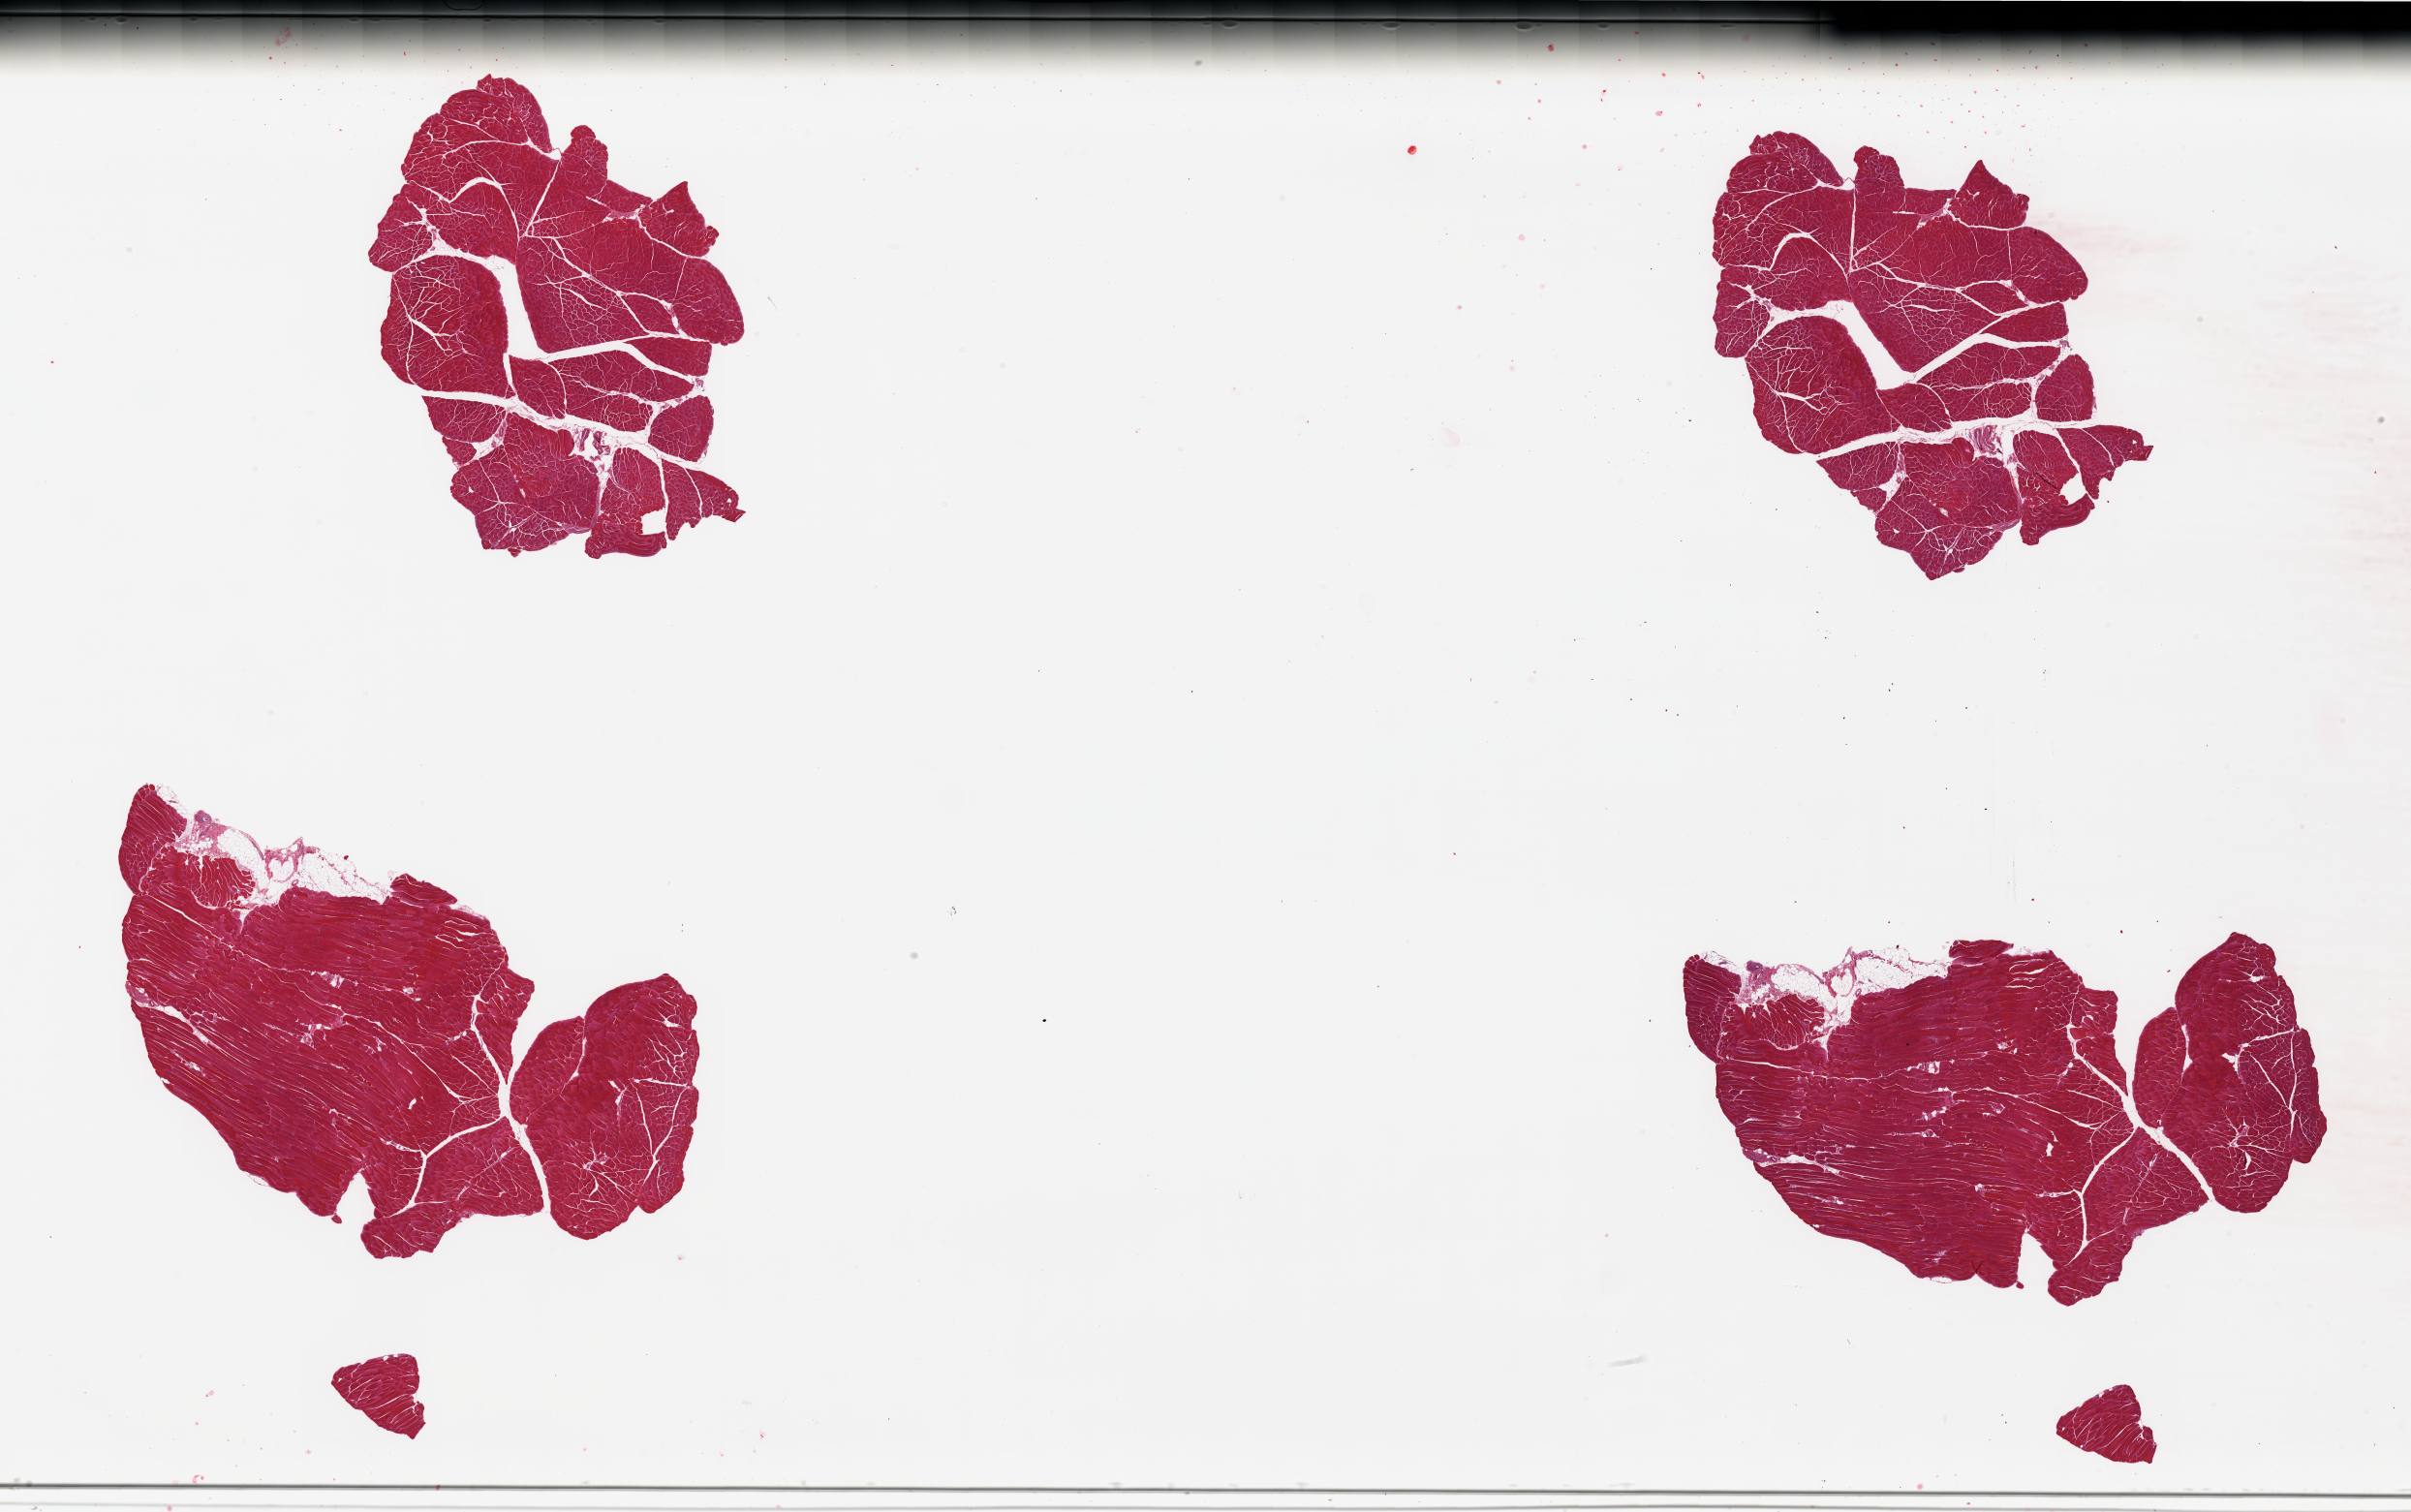
Haematoxylin and eosin whole-slide image, a low-resolution overview of the entire scanned area, about 39.4 x 24.7 mm (slide scanned at 20x), PAXgene-fixed paraffin-embedded (PFPE) section, section of skeletal muscle (target tissue), tissue donor sample. Donor: male.
- pathologist's review note for this sample: 4 pieces, interstitial fat/vascular elements are ~10% of tissue